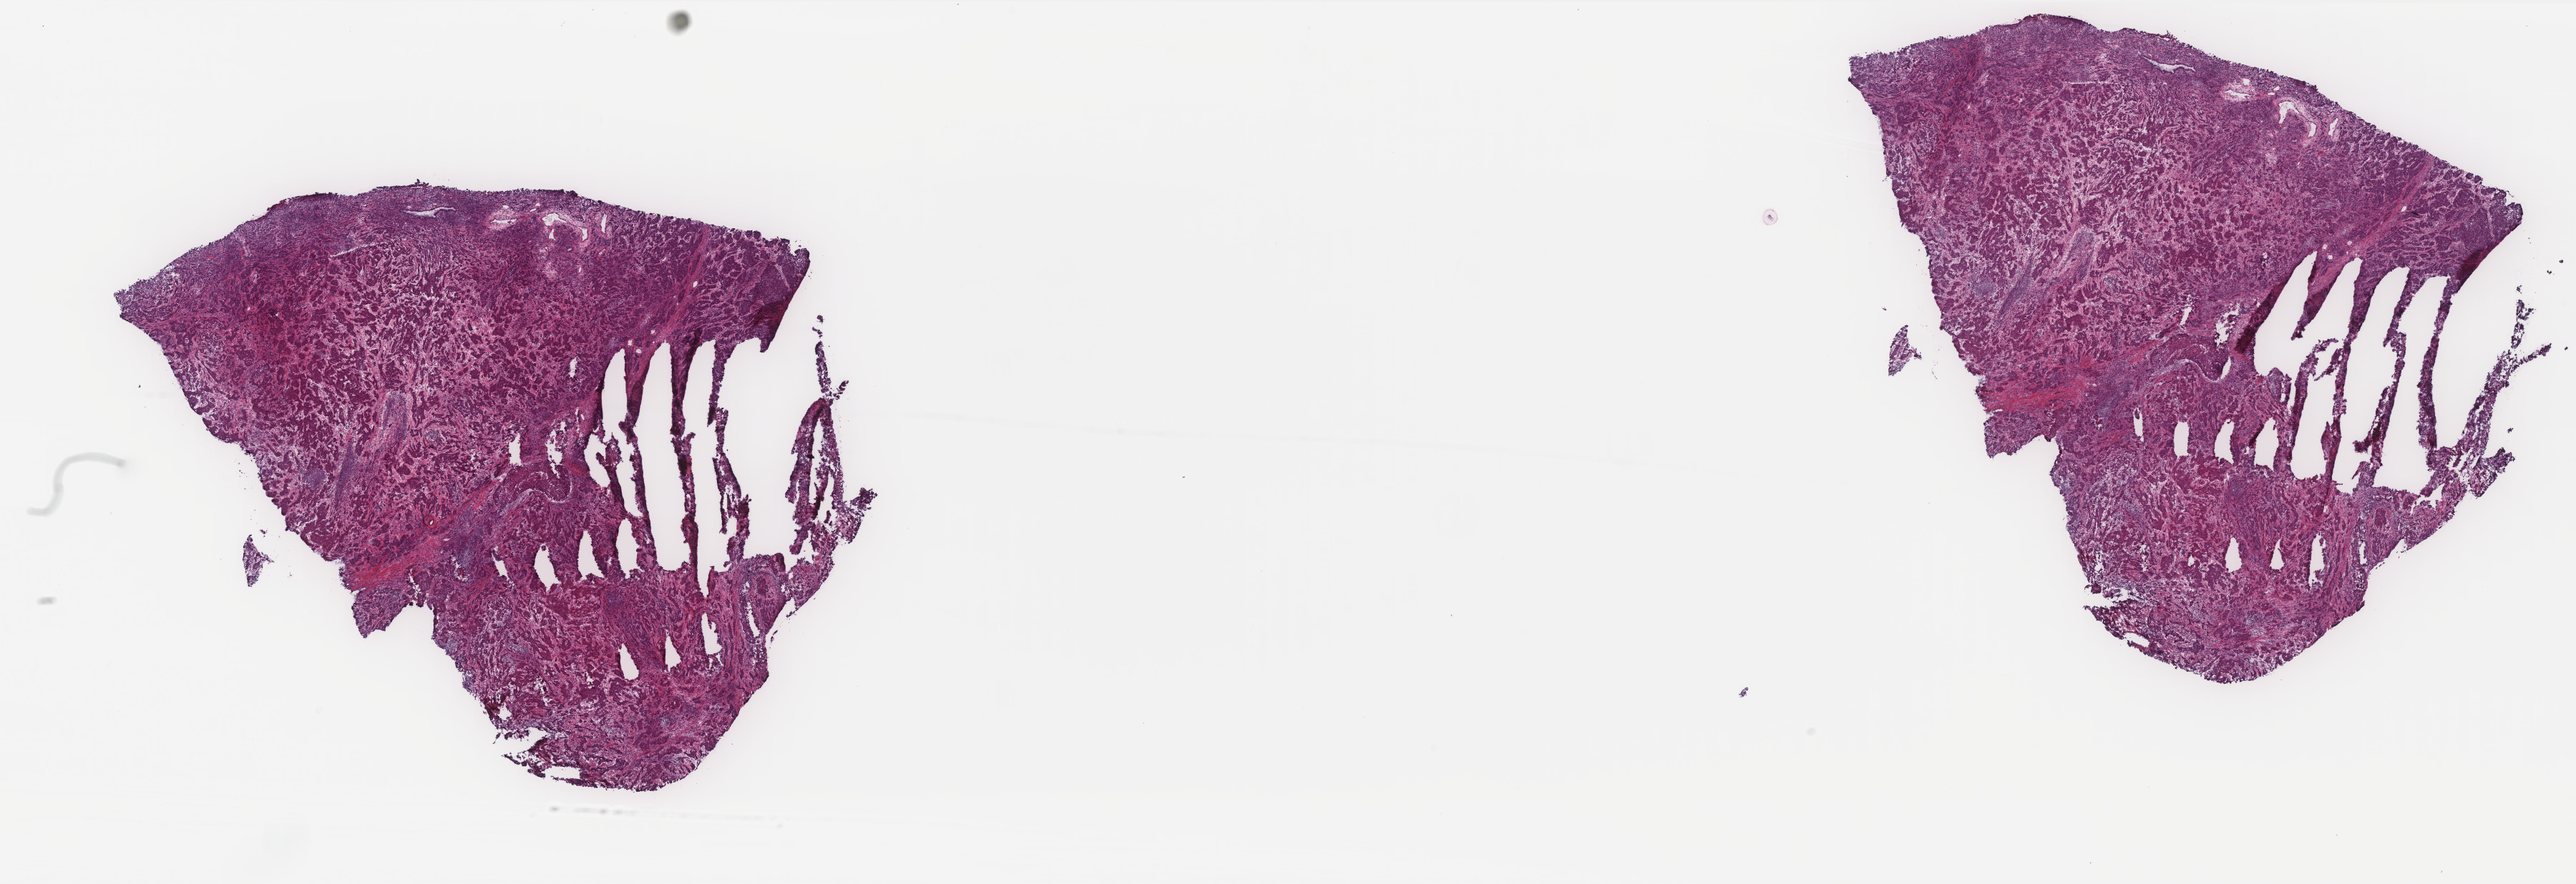
Digitized Hematoxylin and eosin (H&E) stained tissue section (whole slide), a low-resolution overview of the entire scanned area, about 28.9 x 9.9 mm. Frozen section from the top of the tissue portion. Cervix, primary tumour sample. Patient: female, age at initial diagnosis 34 years.
Pathologic diagnosis: Squamous cell carcinoma, NOS (cervix uteri).